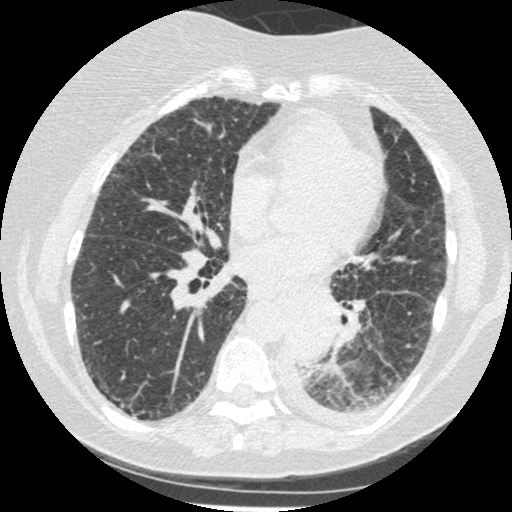
Low-dose screening chest CT, one axial slice; reconstruction kernel STANDARD; 120 kVp; lung window (W 1500 / L -600 HU); 1.25 mm slice thickness; 512 × 512 image matrix, field of view 310 × 310 mm.
Annotated regions visible in this slice (manually delineated by an expert):
- lesion 1 (tumor, lower lobe of left lung): bounding box [x1, y1, x2, y2] px = [286, 306, 338, 363]